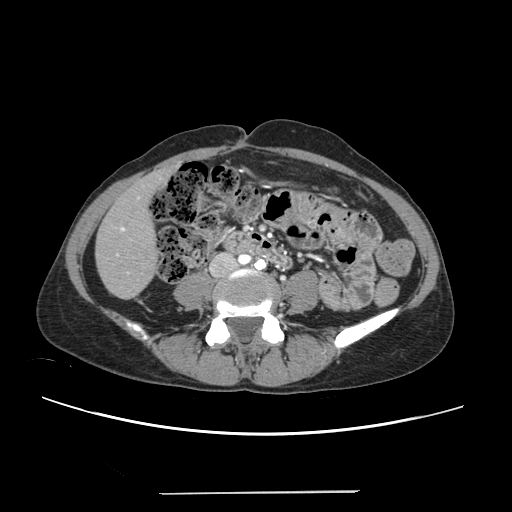
Contrast-enhanced abdominal CT, one axial slice; intravenous contrast given; soft-tissue window (W 400 / L 40 HU); 512 × 512 image matrix. Female patient, age 60 years. From the clinical record (not read from this slice): diagnosis: colorectal cancer liver metastases, imaged before liver resection; multiple liver metastases: no; largest metastasis: 1.5 cm.
Outlined on this slice (manually delineated by an expert):
- liver: box from (x=96, y=170) to (x=171, y=298) px
- planned liver remnant (the part of the liver to remain after resection): (x=96, y=171)–(x=168, y=298)
- portal vein (with intrahepatic branches): (x=116, y=196)–(x=140, y=274)